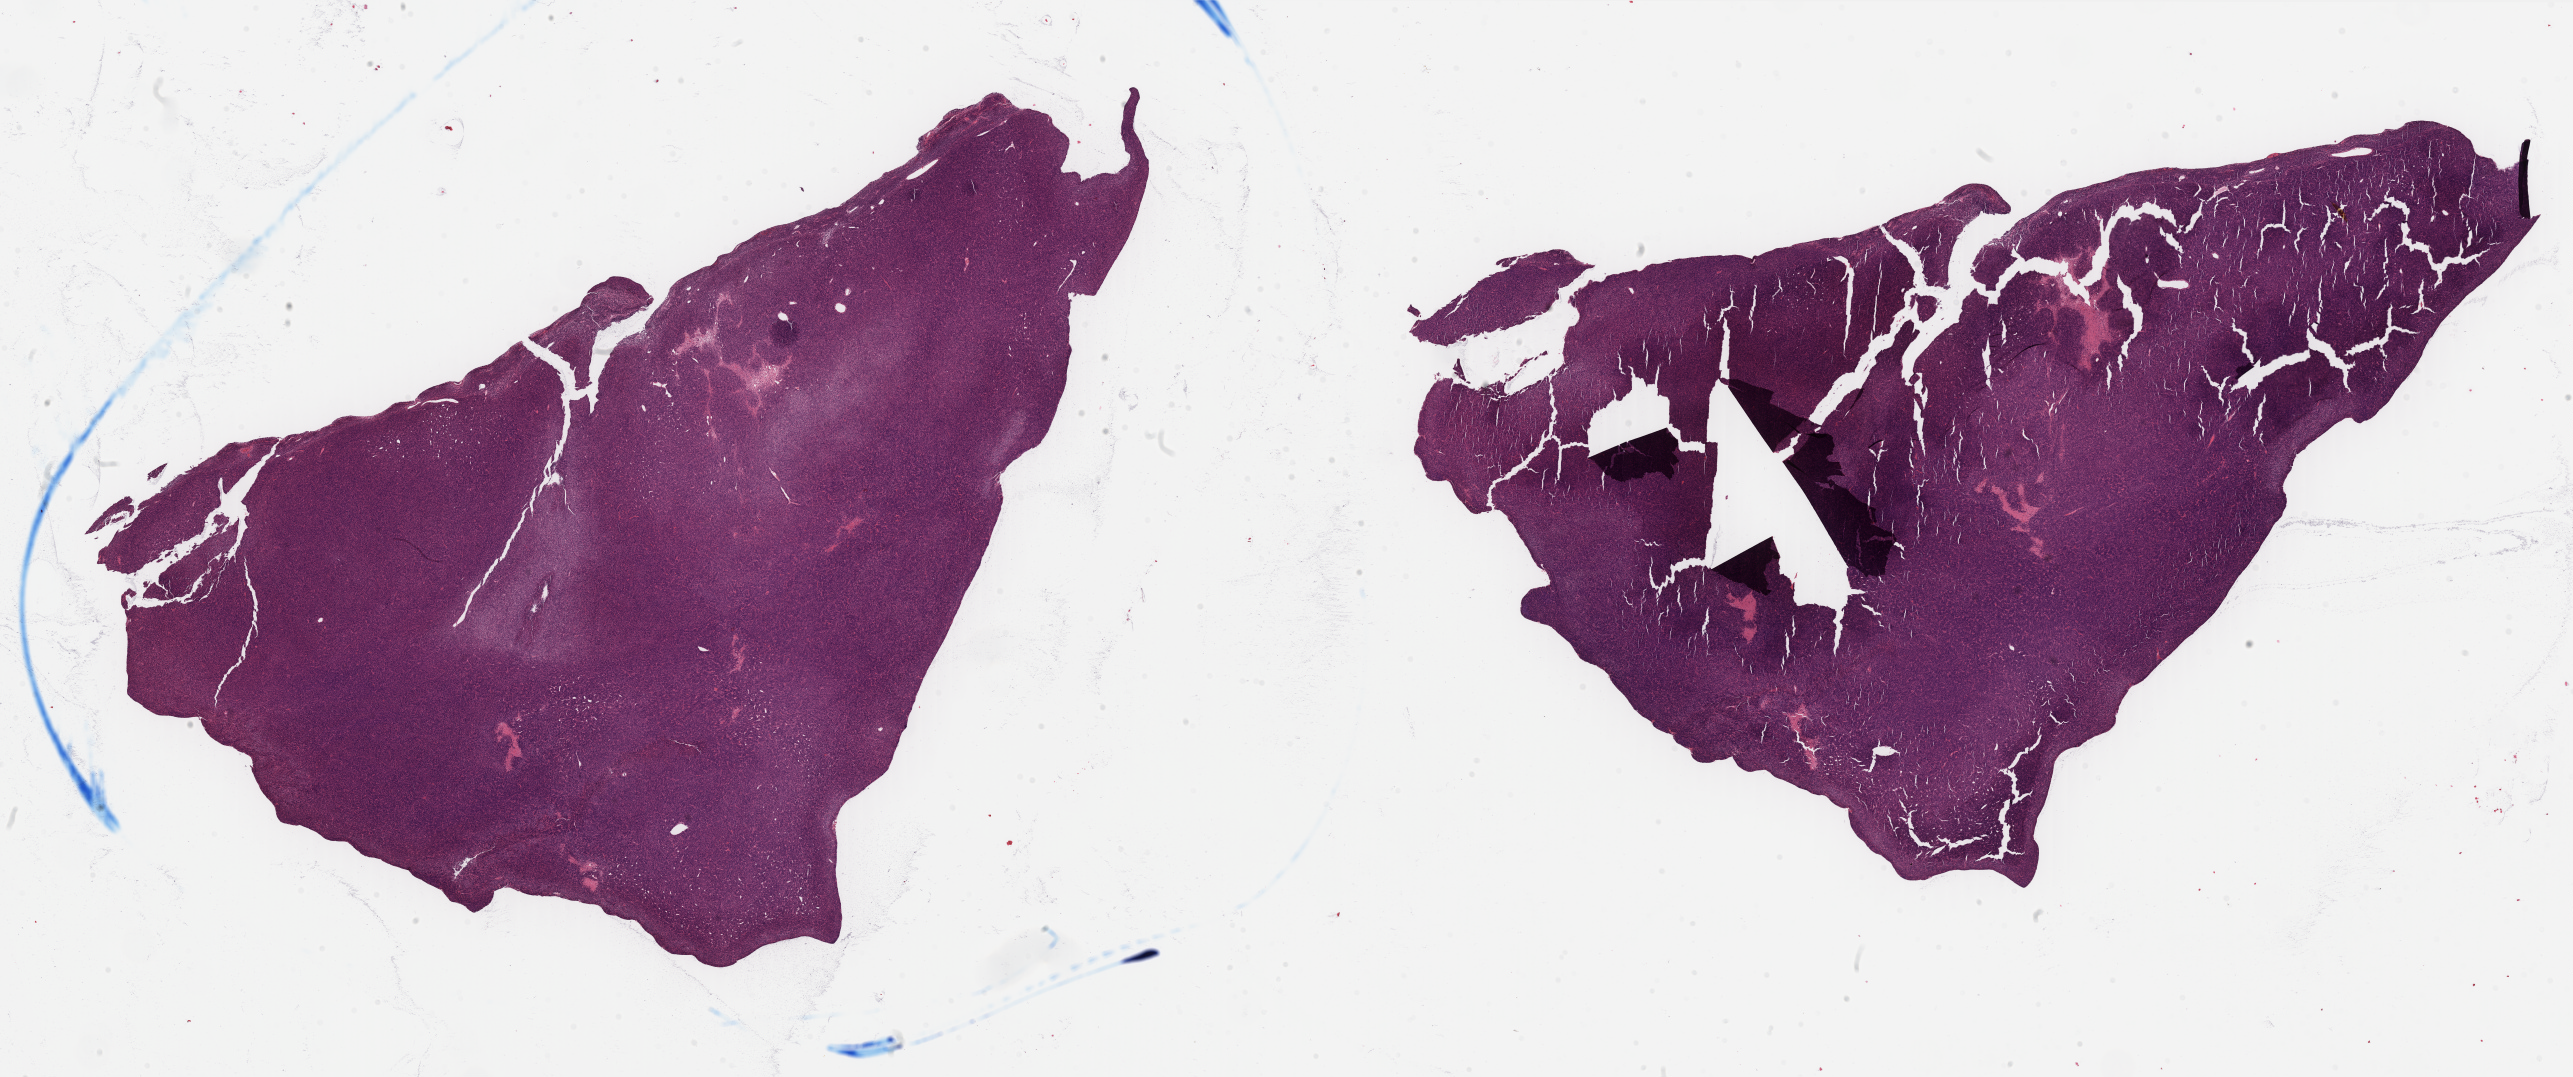
Digitized H&E-stained tissue section (whole slide), whole scanned area (about 40.7 x 17.0 mm, slide scanned at 40x) shown as a low-resolution overview, FFPE section, sample: primary tumour, uterus. Female, age 46 years at initial diagnosis.
Histologic diagnosis: Leiomyosarcoma, NOS.